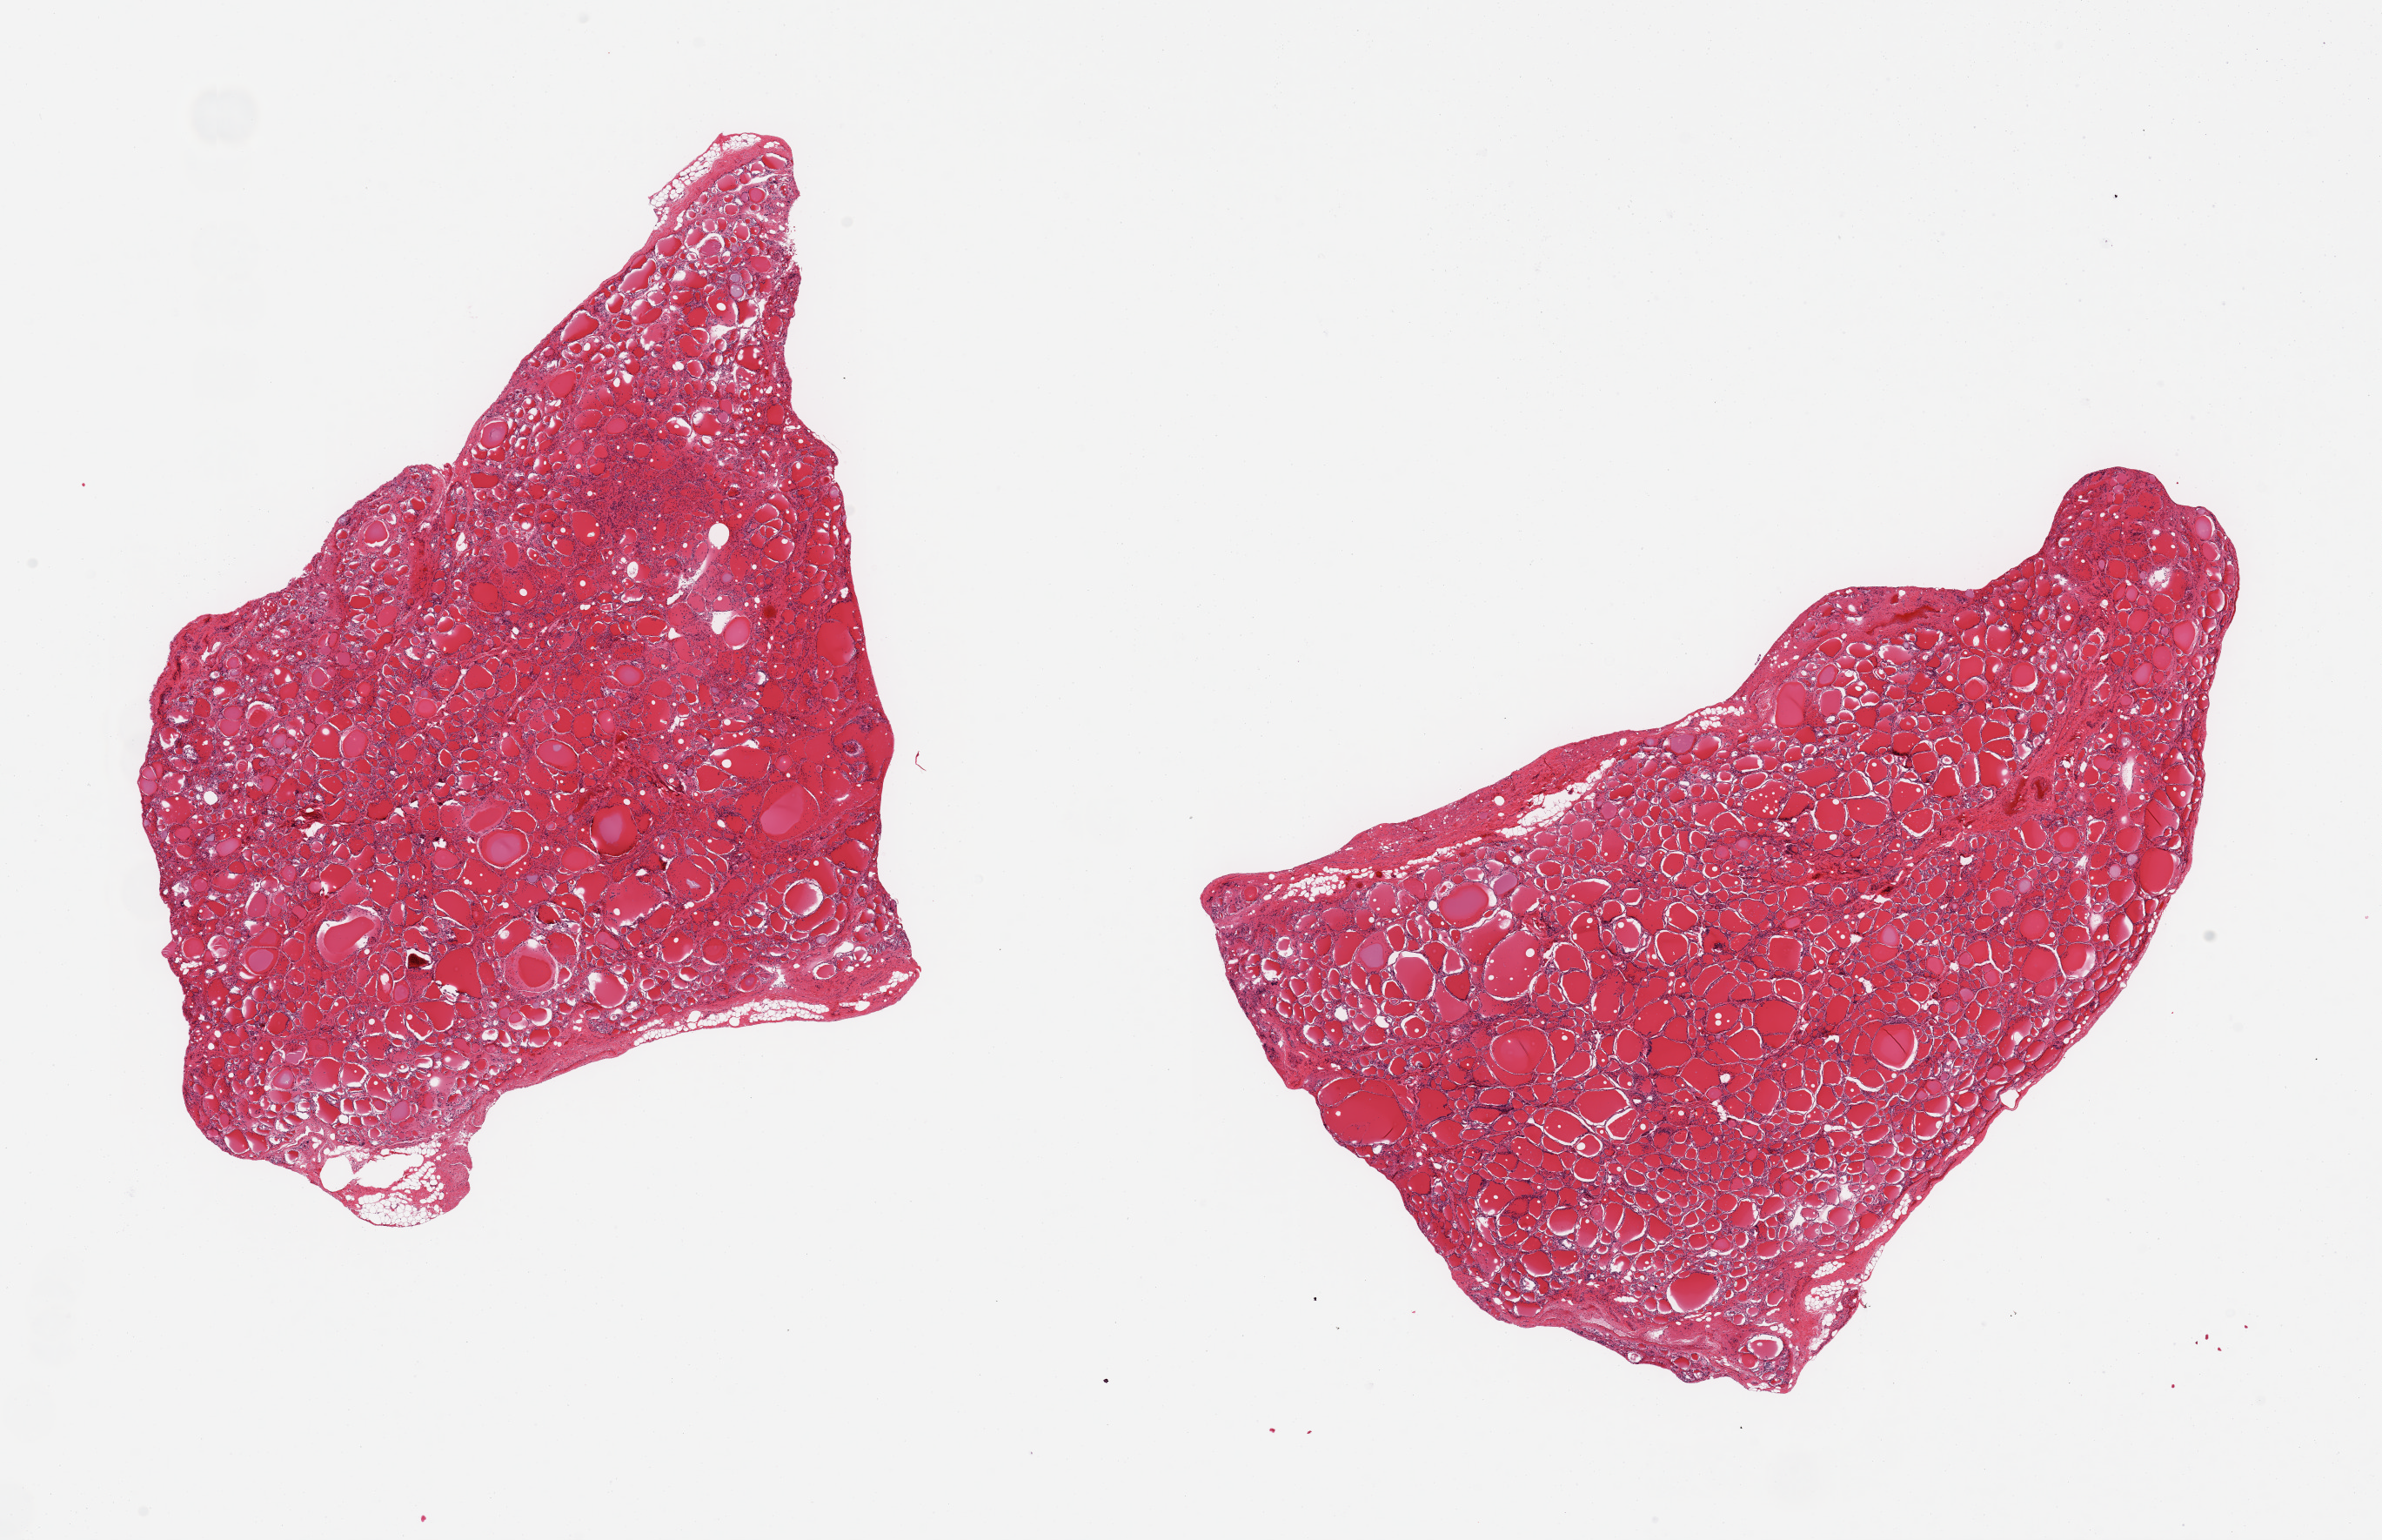
Whole-slide image, haematoxylin and eosin stain, brightfield, shown as a low-resolution overview of the whole scanned area (about 21.7 x 14.0 mm); PAXgene-fixed paraffin-embedded (PFPE) section; target tissue: thyroid; tissue donor sample. Donor: female.
Review note (as recorded): 2 pieces; <5% external fibrofatty component.